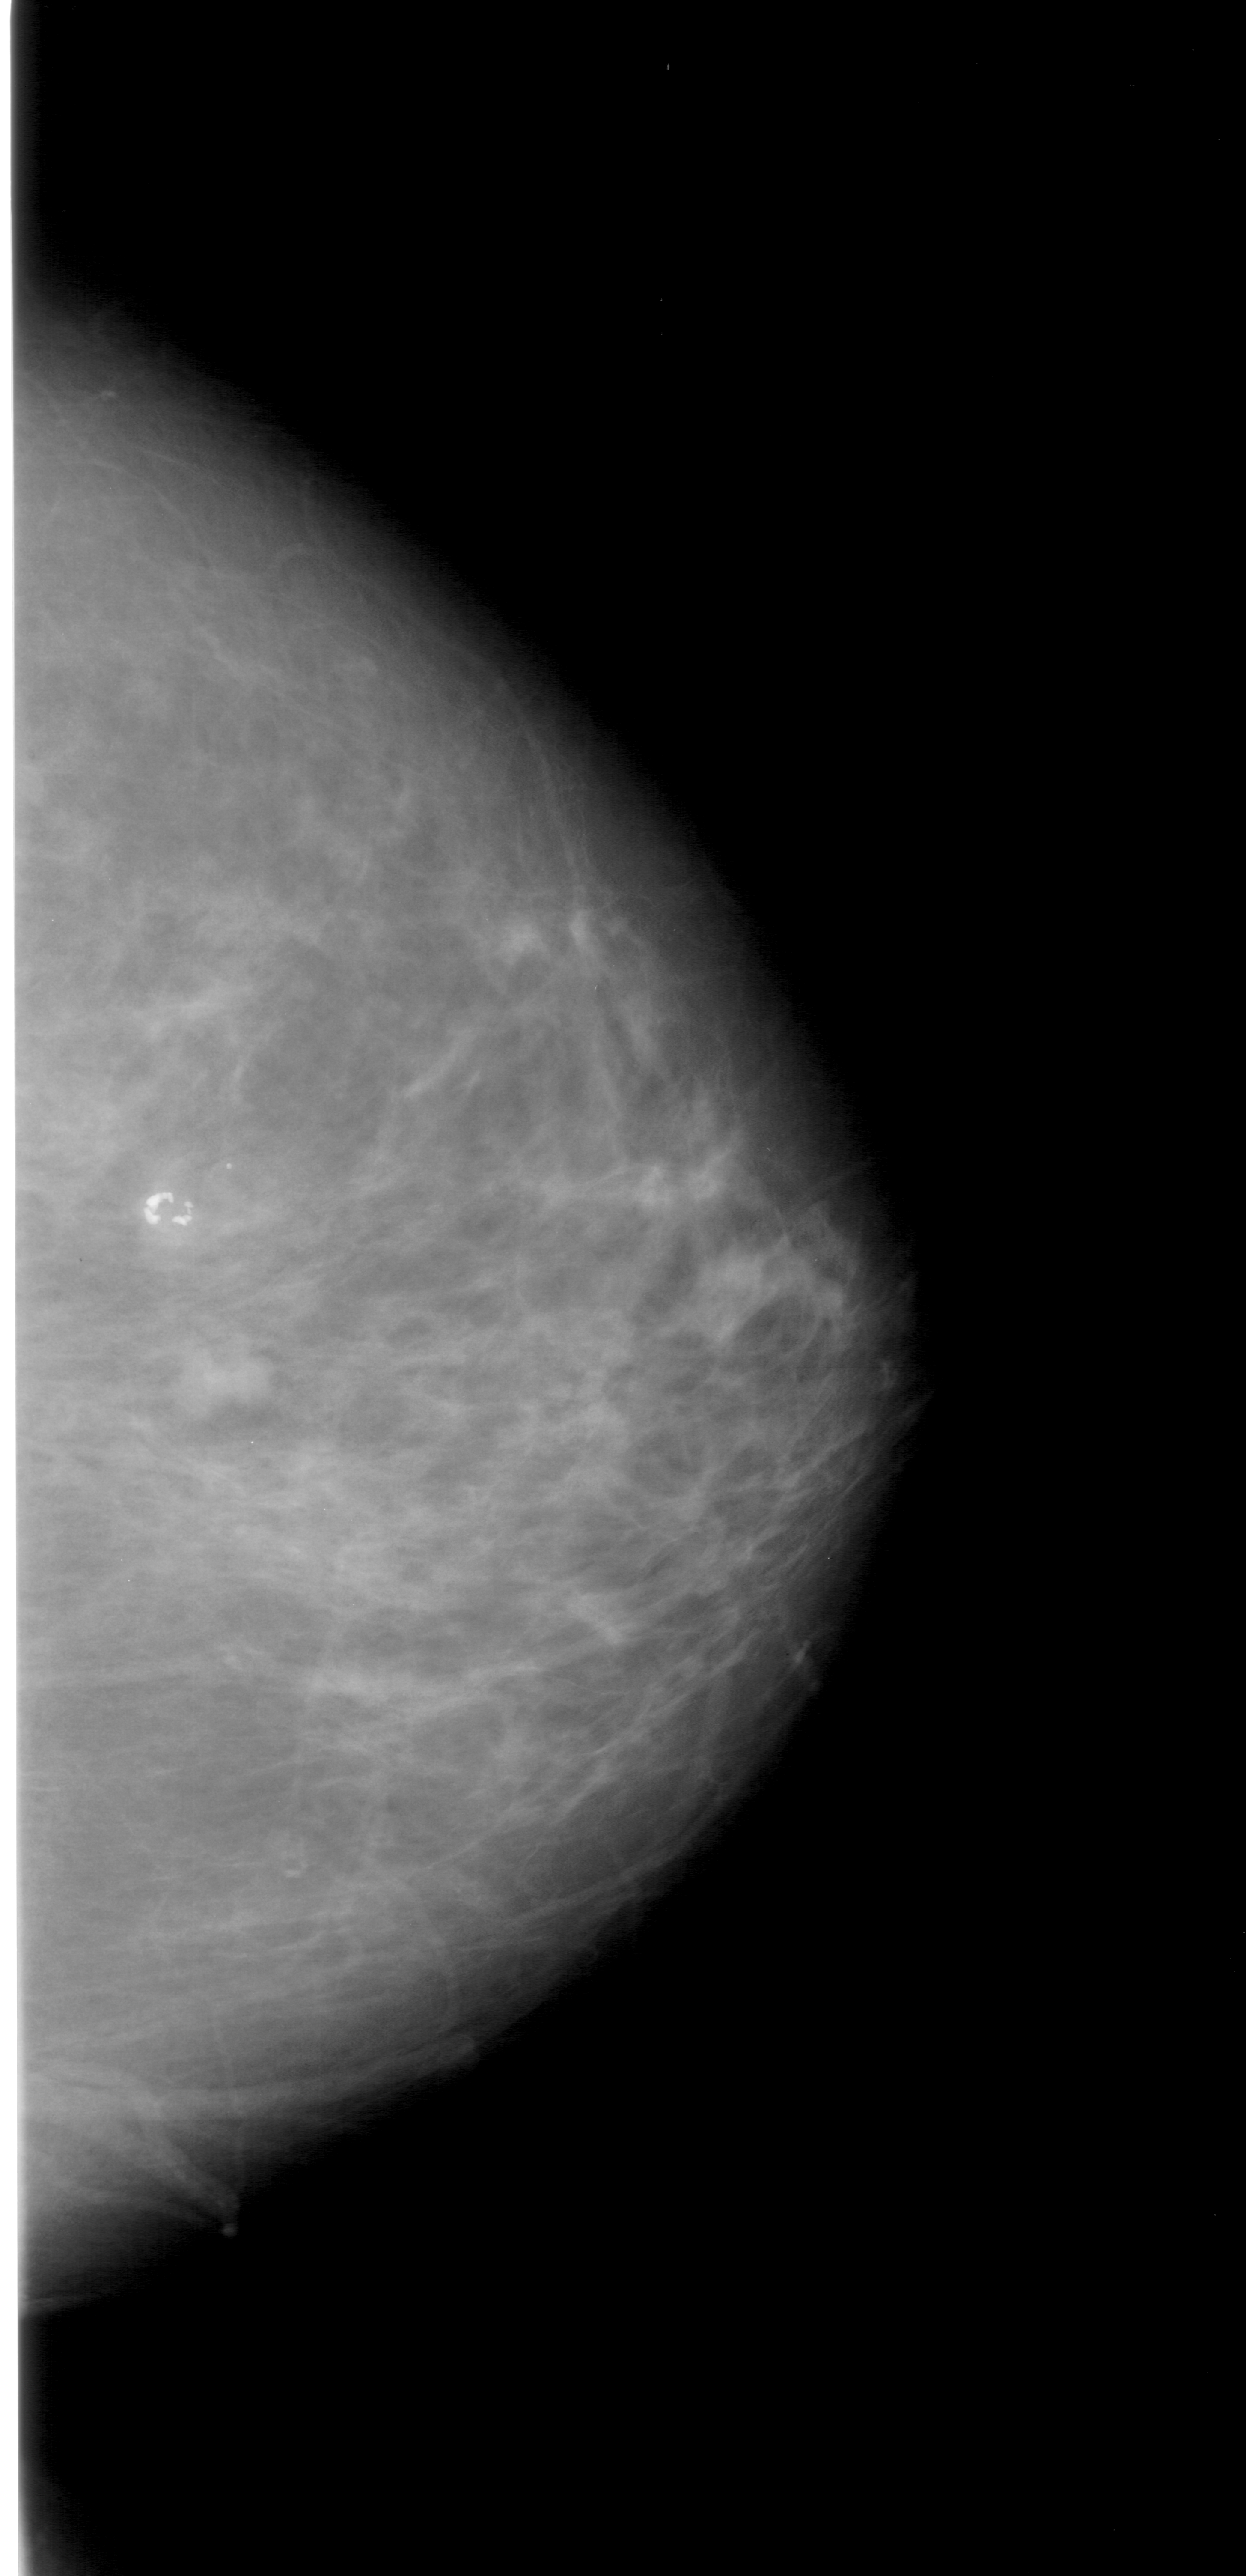
Scanned film-screen mammogram; right breast; craniocaudal (CC) view; BI-RADS breast density category 3 (scale 1–4); 1246 × 2576 image matrix.
Marked abnormalities (boxes around the expert regions of interest):
- mass, shape lobulated, margins ill defined; BI-RADS assessment category 4; subtlety rating 1 on a 1 (subtle) to 5 (obvious) scale; pathology (as recorded): malignant: bounding box <187,1329,281,1412> (left, top, right, bottom; pixels)